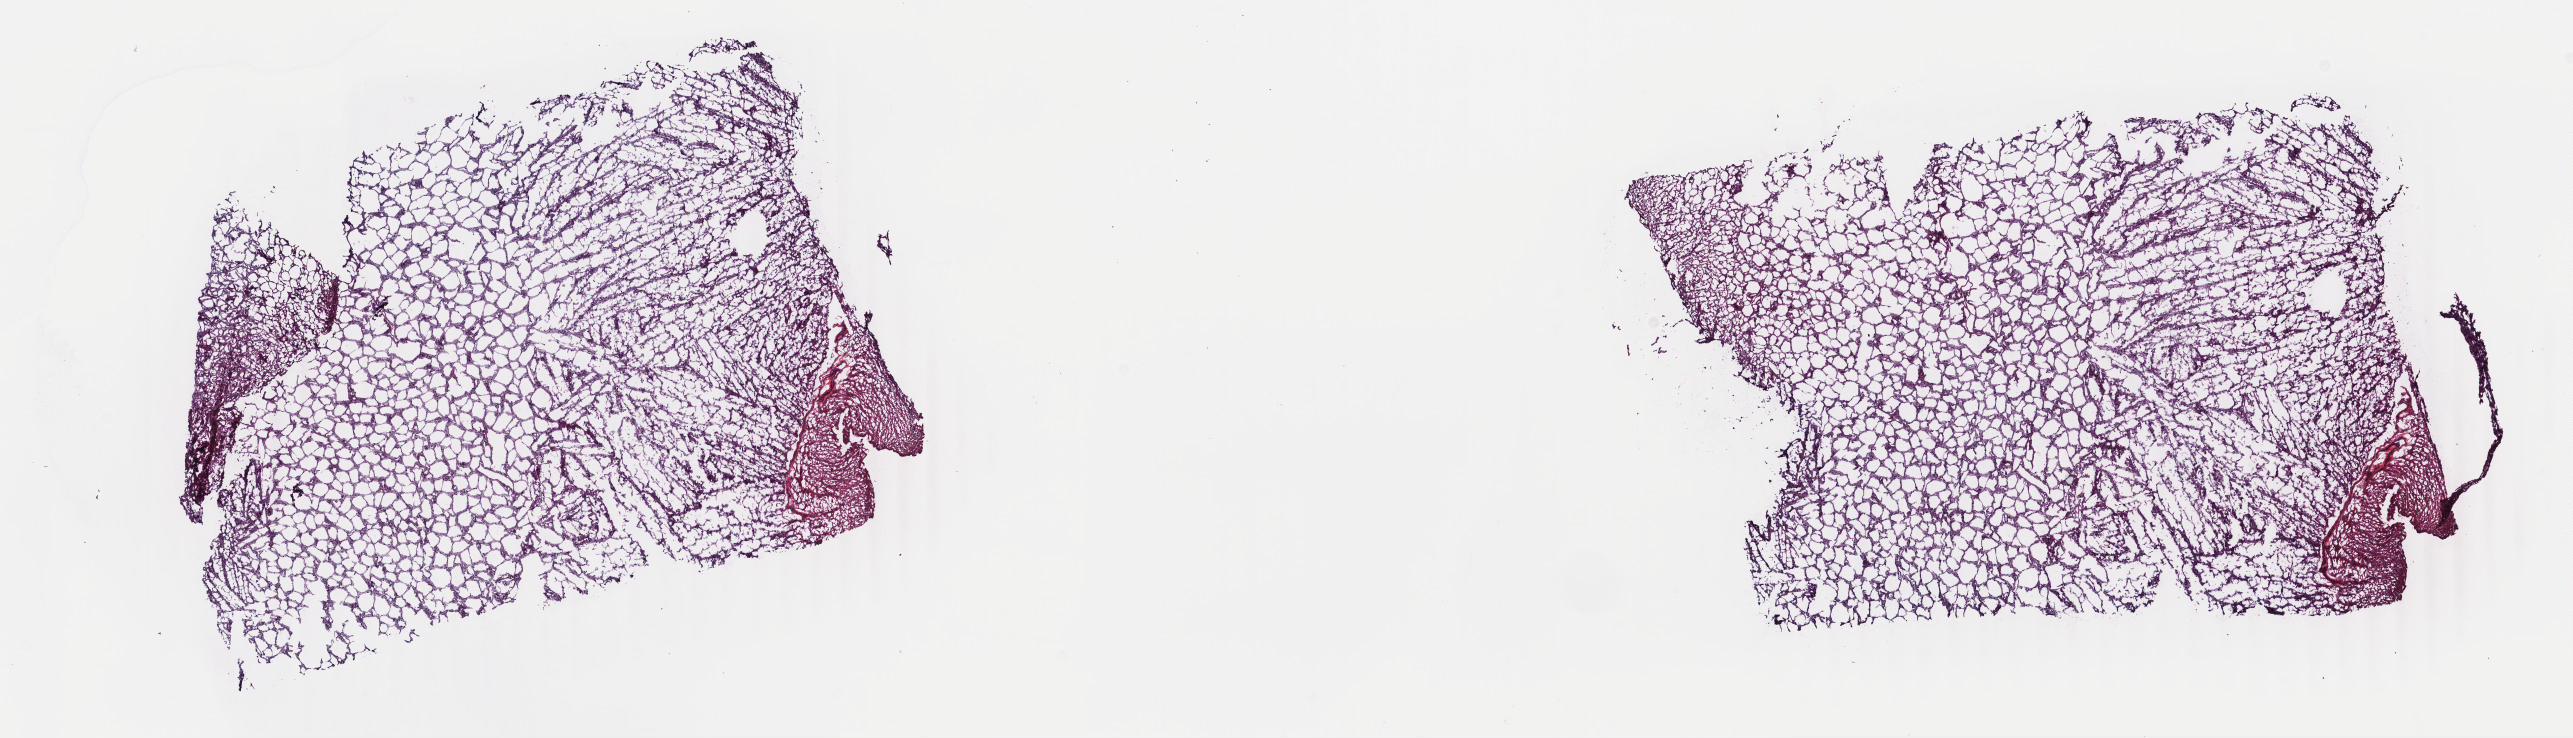
Digitized H&E tissue section (whole slide) — a low-resolution overview of the entire scanned area, about 20.5 x 5.9 mm. Frozen section from the top of the tissue portion. Primary tumour sample from the brain. Patient: male, age at initial diagnosis 47 years. Histologic grade: G2 (moderately differentiated). Pathologist review of this section (percent, as recorded): tumour cells 80%, tumour nuclei 80%, normal cells 20%, stromal cells 0%, necrosis 0%. Infiltration values recorded for this section: lymphocyte infiltration 0%, monocyte infiltration 0%, neutrophil infiltration 0%.
Laterality: right. Histologic diagnosis: Astrocytoma, NOS (frontal lobe).